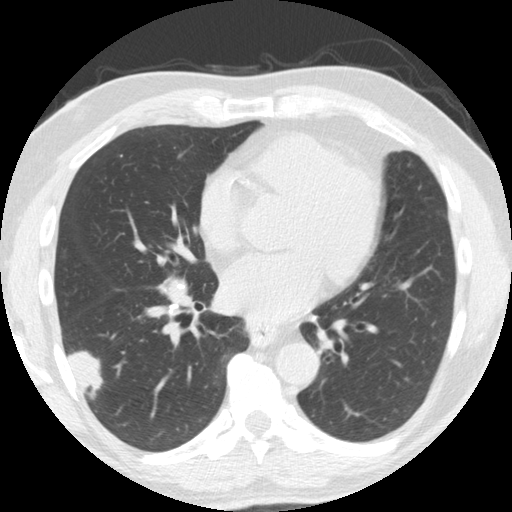
Low-dose screening chest CT, one axial slice. Slice 78 of 174 in the series (ordered by position). 120 kVp. Lung window (W 1500 / L -600 HU). 2.5 mm slice thickness. 512 × 512 image matrix.
Annotated regions visible in this slice (manually delineated by an expert):
- lesion 1 (tumor, lower lobe of right lung): bounding box (x1, y1, x2, y2) in pixels: (68, 351, 103, 392)